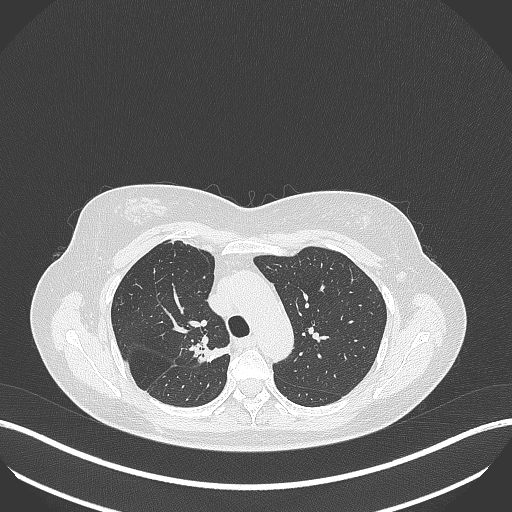
Chest CT, one axial slice; position 282 of 386 along the scan axis; reconstruction kernel B70f; 120 kVp; lung window (W 1500 / L -600 HU); 512 × 512 image matrix, field of view 400 × 400 mm. Female patient, age 65 years. Case-level facts recorded for this patient, not image findings: clinical TNM (as recorded): T1b N0 M0.
Annotated regions visible in this slice (rectangle marked by the reading radiologist):
- lung tumour (recorded histology: adenocarcinoma): bounding box <185,338,231,366> (left, top, right, bottom; pixels)